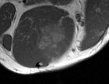
MRI of an extremity soft-tissue mass, one axial slice; slice 39 of 50 in the series (ordered by position); MR volume resampled by the dataset authors to the PET/CT grid (not the native acquisition matrix); 109 × 84 image matrix, field of view 106 × 82 mm. Male patient. Case-level facts recorded for this patient, not image findings: histological type: synovial sarcoma; site of the primary tumour: left poplietal fossa.
Structures marked on this image (expert contour drawn on MRI and transferred to this co-registered scan by the dataset authors):
- gross tumour volume (mass): bounding box <34,26,63,61> (left, top, right, bottom; pixels)